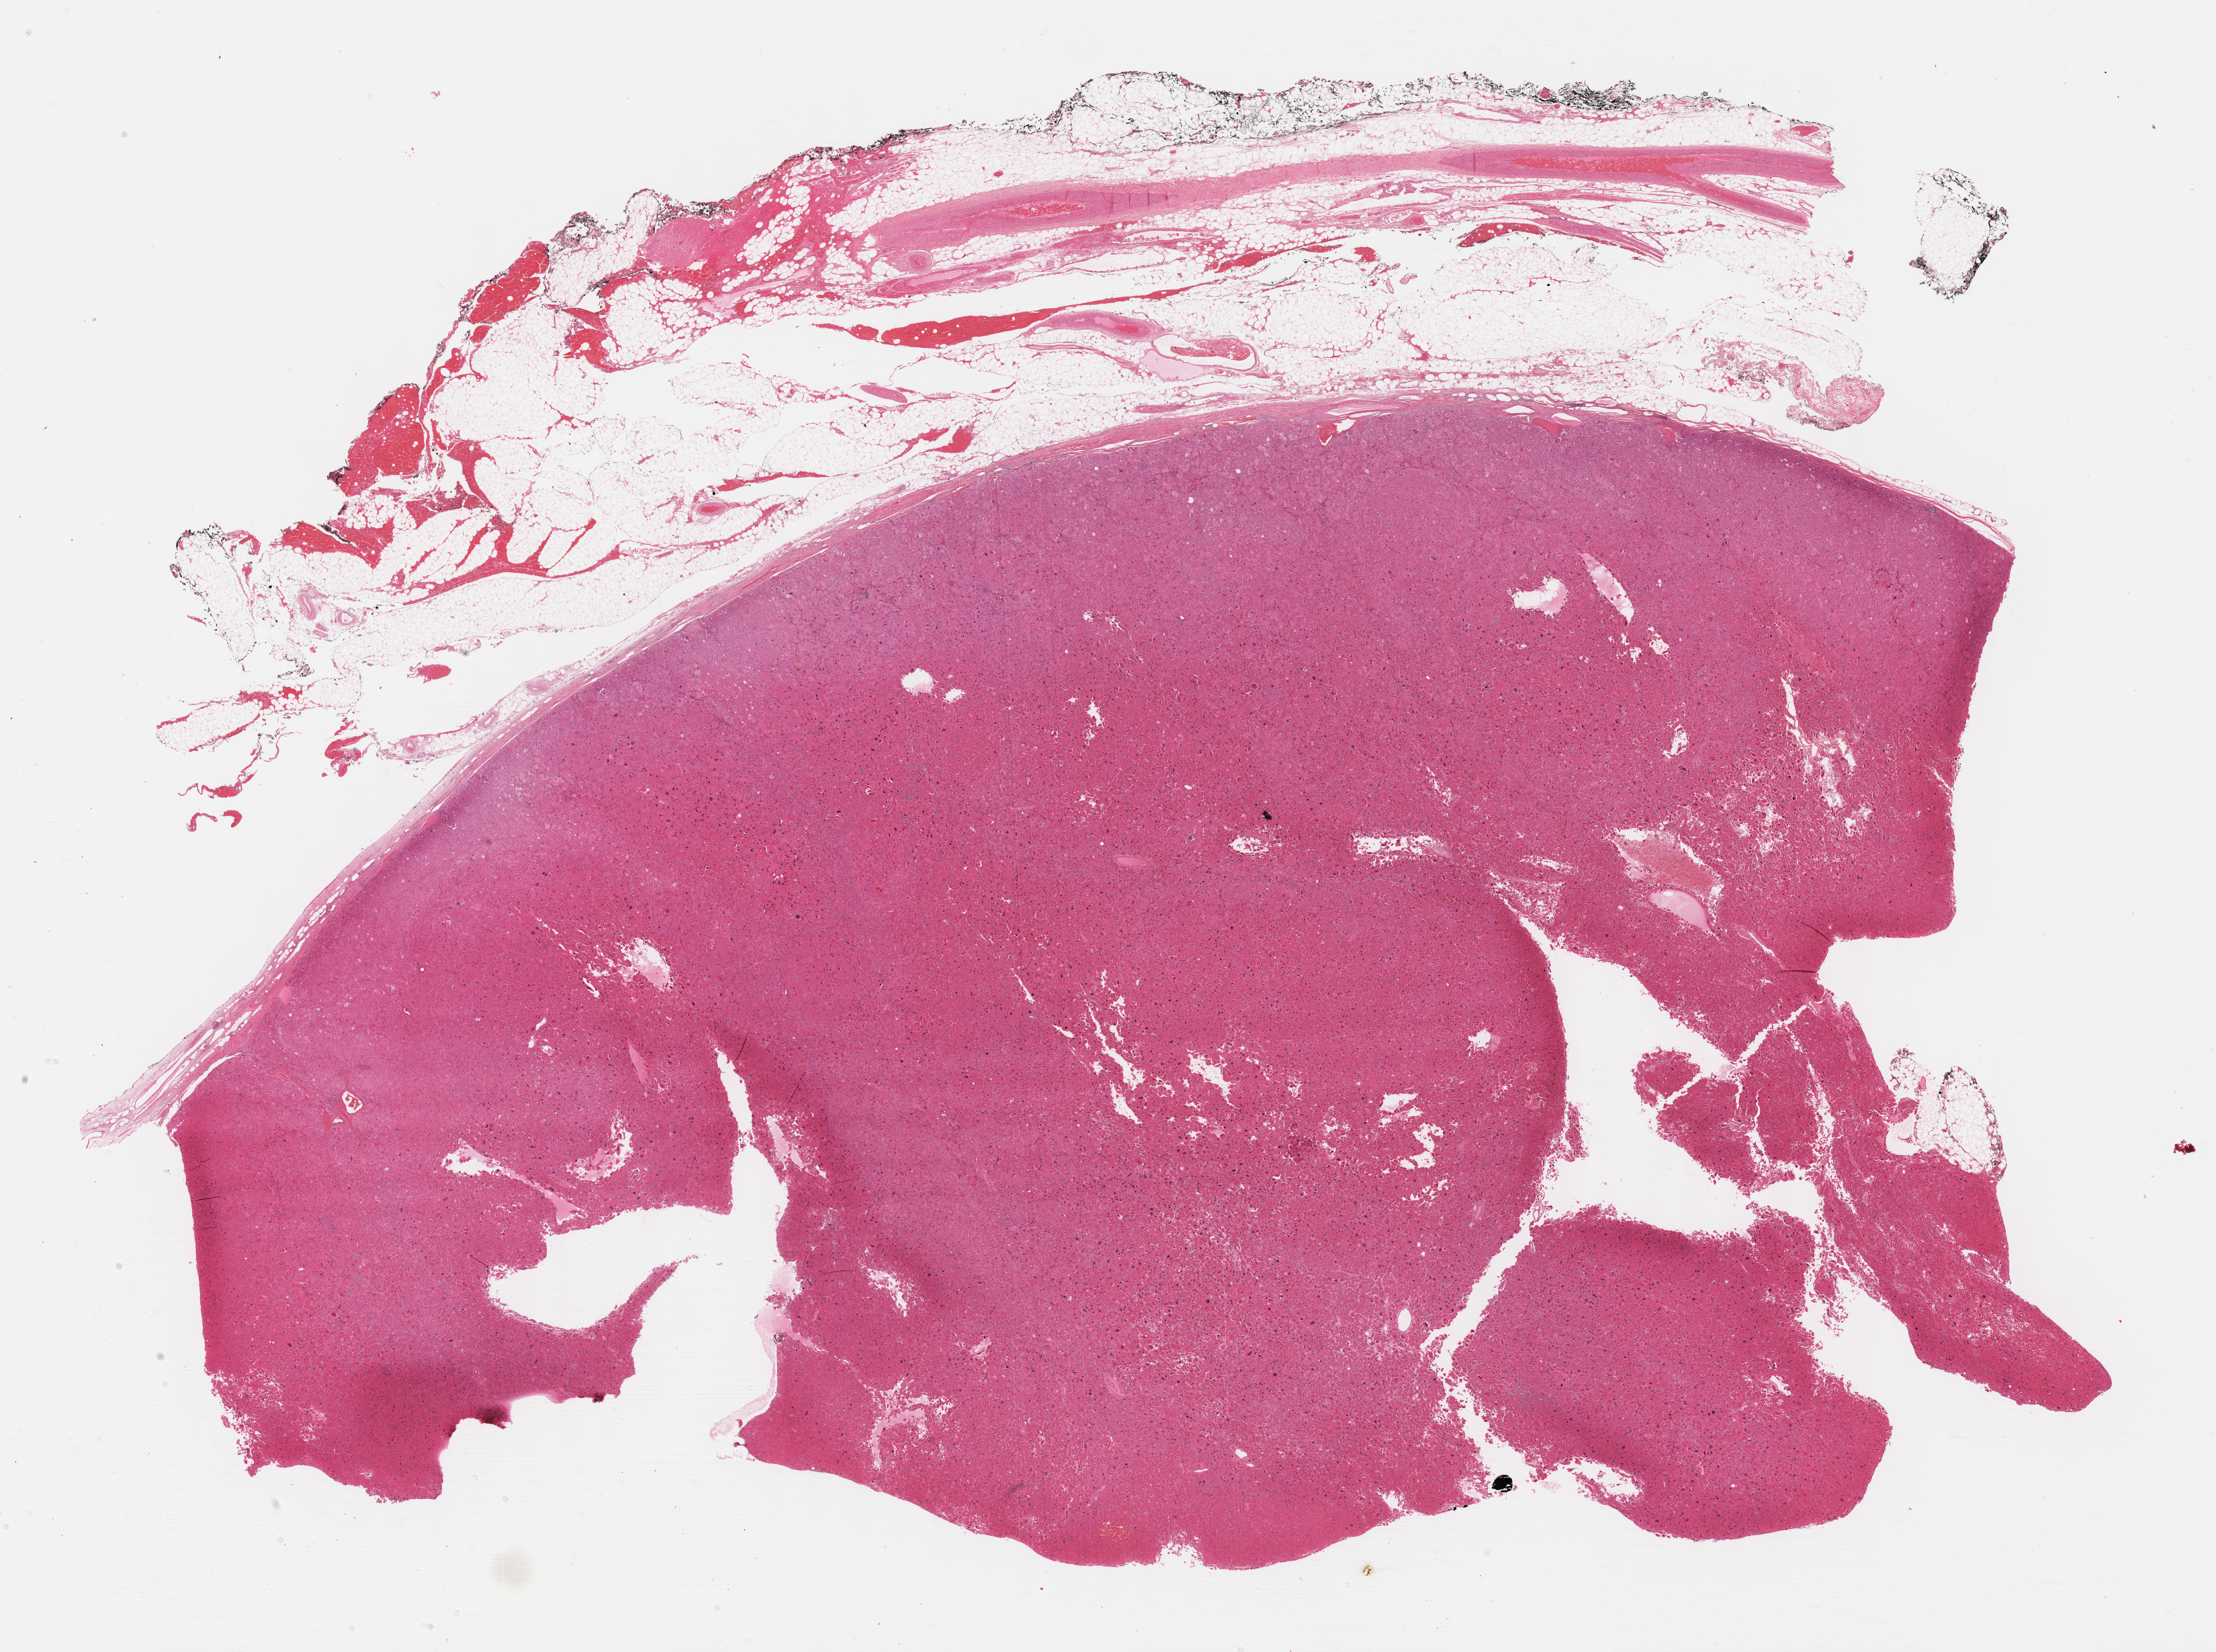
Digitized H&E tissue section (whole slide), low-resolution overview of the scanned area, about 26.7 x 19.9 mm (acquisition: 40x scan). Formalin-fixed paraffin-embedded (FFPE) diagnostic section. Adrenal cortex, primary tumour sample. Female, age 57 years at initial diagnosis.
Diagnosis: Adrenal cortical carcinoma (cortex of adrenal gland).